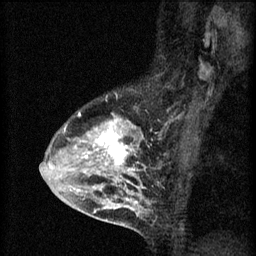
Breast MRI (dynamic contrast-enhanced), one sagittal slice. Position 42 of 60 along the scan axis. 3 images stored at this slice position (order not interpretable as contrast timing). 1.5 T. TE 4.2 ms, TR 8.2 ms. 2 mm slice thickness. 256 × 256 image matrix. Patient: female, 45 years.
Annotated regions visible in this slice (semi-automatic segmentation, software-assisted and operator-edited):
- analysis volume of interest (the breast-tissue region the enhancement analysis was run in; not a lesion): box from (x=54, y=112) to (x=151, y=217) px
- tumour enhancement mask (voxels above the 70 % enhancement threshold inside the analysis volume of interest): (x=62, y=112)–(x=143, y=217)